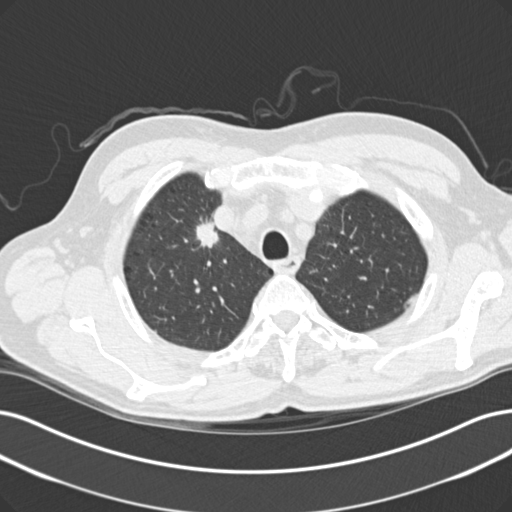
Low-dose screening chest CT, one axial slice. Slice 122 of 152 in the series (ordered by position). Lung window (W 1500 / L -600 HU). 2 mm slice thickness. 512 × 512 image matrix, field of view 365 × 365 mm.
Structures marked on this image (manually delineated by an expert):
- lesion 1 (tumor, upper lobe of right lung): box from (x=196, y=219) to (x=219, y=248) px